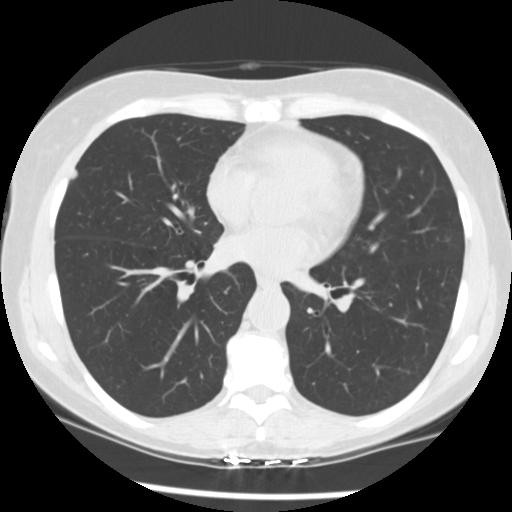
Low-dose screening chest CT, one axial slice. Slice 125 of 241 in the series (ordered by position). Reconstruction kernel STANDARD. 120 kVp. Lung window (W 1500 / L -600 HU). 512 × 512 image matrix.
Structures marked on this image (manually delineated by an expert):
- lesion 1 (tumor, upper lobe of right lung): box from (x=72, y=169) to (x=76, y=178) px